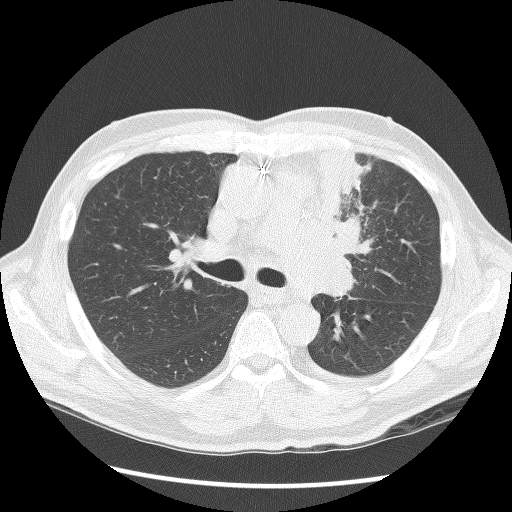
Low-dose screening chest CT, axial slice; second screening round (one year after baseline); lung window (W 1500 / L -600 HU); 2.5 mm slice thickness; 120 kVp; 512 × 512 image matrix. Male, age 64 years at enrolment. Former smoker at enrolment.
• Expert-annotated lung lesion, bounding box [x1, y1, x2, y2] px = [301, 151, 380, 285].
• No non-calcified nodule or mass ≥4 mm was recorded by the screening reader at this exam.
• Official screen result: positive, other.
• Later outcome: lung cancer diagnosed 24 days after this screen — small cell carcinoma, NOS, left upper lobe, stage IV (AJCC 6th edition), 100 mm at pathology.